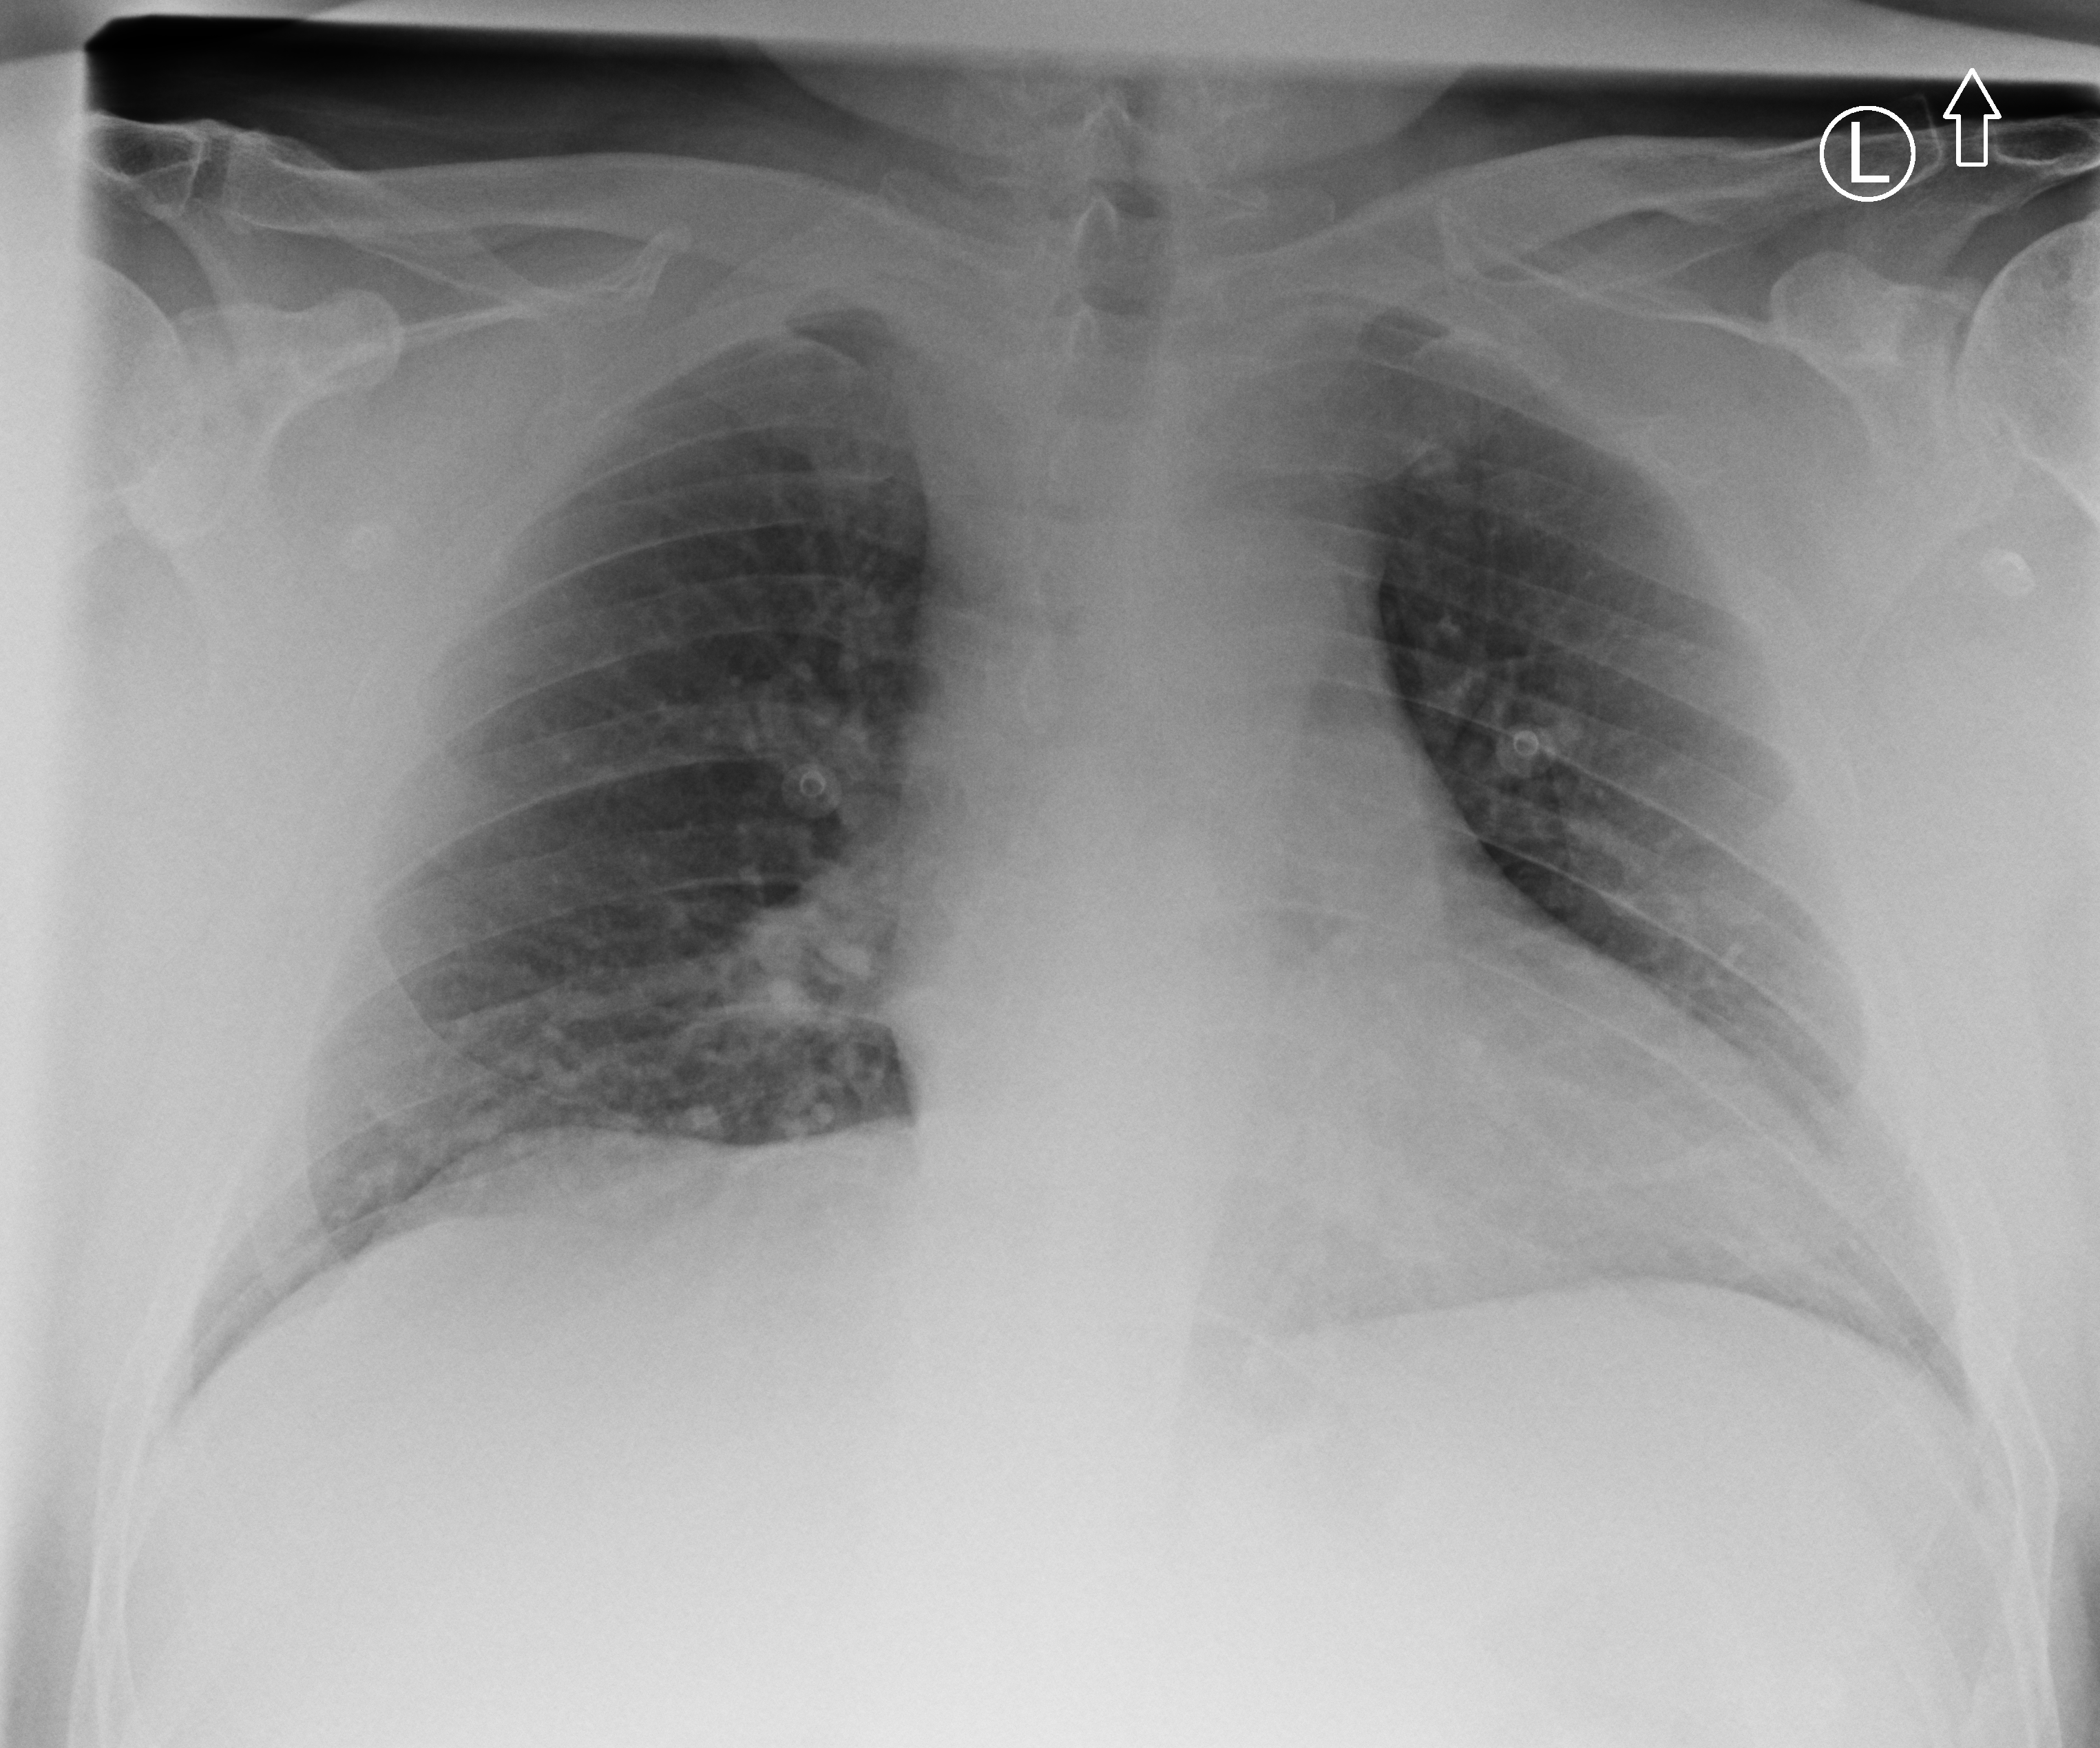
Bedside chest radiograph (computed radiography); anteroposterior (AP) projection. Male patient hospitalised with COVID-19, age 18–59 years.
From the hospital-stay record, not from the radiograph (when in the stay this image was taken is not recorded): mechanically ventilated during this hospital stay: no.